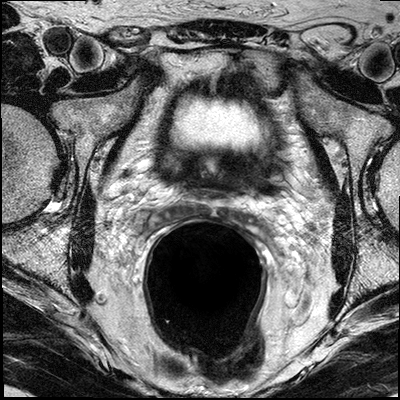
Multiparametric prostate MRI examination; 3 images, each a single mid-volume slice chosen by position (not for content). Treatment context recorded for this patient: No surgery, active surveillance.
Image 1: axial T2-weighted image, slice 17 of 32.
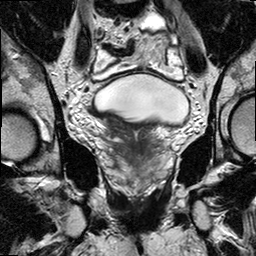
Image 2: T2-weighted coronal slice, slice 13 of 24, 3 mm slice thickness.
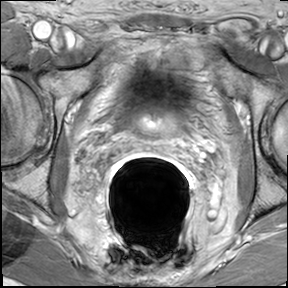
Image 3: axial dynamic contrast-enhanced (DCE) T1-weighted image, series "AX BLISS_GAD", slice 17 of 32, dynamic phase 4 of 7, 6 mm slice thickness.
MRI report (verbatim):
The prostate has a maximal lateral diameter of 5.5 cm, a maximal craniocaudal diameter of 4.1 cm and a maximal AP diameter of 3.2 cm resulting in an estimated gland volume of 38 cc. The zonal anatomy is preserved. There is diffuse linear (centrifugal configured) enhancement throughout the prostate, suggestive for marked chronic prostatitis. Slightly obscured by the enhancement pattern of the chronic prostatitis, there are several small foci of suspicious enhancement in the mid prostate and prostate base, in the right and left peripheral zone - compatible with small cancer foci. No foci larger than 5 mm. (the largest in the right upper posterior lateral peripheral zone with a max diameter of 5 mm) There is minimal BPH. No evidence for involvement of the neurovascular bundle on either side. No evidence for seminal vesicles infiltration. No evidence of involvement of bladder neck and rectal wall. No suspiciously enlarged obturator and iliac lymph nodes. Diffuse patchy and geographic signal change of the visualized osseus structures on the T1-weighted images (hypo-intense), less likely associated with prostate cancer. Clinical correlation and bone scan recommended for further evaluation. IMPRESSION: 1) Possible multifocal bilateral prostate cancer with small sub 5 mm foci. No evidence of local extraprostatic disease. 2) Marked Chronic prostatitis. 3) Mild BPH. 4) Diffuse patchy and geographic signal change of the visualized osseus structures (pelvic ring, spine) on the T1-weighted images, less likely associated with prostate cancer. Clinical correlation and bone scan recommended for further evaluation.

Prostate biopsy pathology (as recorded):
PROSTATE, LEFT BASE: PROSTATE TISSUE, NO TUMOR IDENTIFIED. B. PROSTATE, LEFT MIDDLE: PROSTATE TISSUE, NO TUMOR IDENTIFIED. C. PROSTATE, LEFT APEX: PROSTATE TISSUE, NO TUMOR IDENTIFIED. D. PROSTATE, RIGHT BASE: PROSTATIC ADENOCARCINOMA, GLEASON GRADE 3+3=6/10 INVOLVING ONE BIOPSY CORE (25% OF TISSUE). E. PROSTATE, RIGHT MIDDLE: PROSTATIC ADENOCARCINOMA, GLEASON GRADE 3+3=6/10 INVOLVING ONE BIOPSY CORE (20% OF TISSUE). F. PROSTATE, RIGHT APEX: PROSTATE TISSUE, NO TUMOR IDENTIFIED.
PROSTATE BIOPSIES (A AND B): A. PROSTATE, LEFT, CORE NEEDLE BIOPSIES: PROSTATIC ADENOCARCINOMA, GLEASON GRADE 3+3=6/10 INVOLVING ONE BIOPSY CORE (5% OF TISSUE). IMMUNOPEROXIDASE STAINS (HMWK) AT OUTSIDE HOSPITAL CONFIRMS DX. B. PROSTATE, RIGHT, CORE NEEDLE BIOPSIES: ATYPICAL SMALL ACINAR PROLIFERATION.